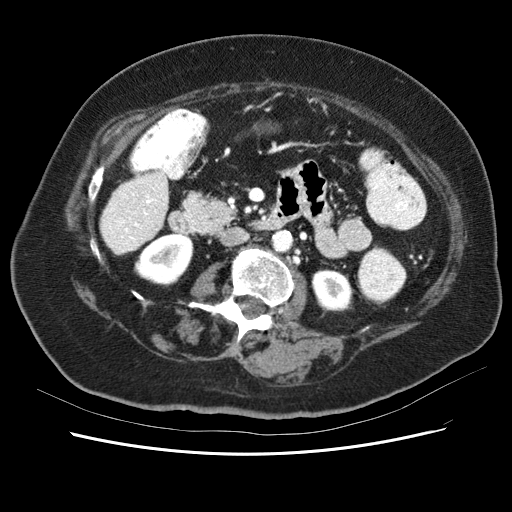
Contrast-enhanced abdominal CT (liver protocol), one axial slice; position 13 of 62 along the scan axis; 120 kVp; soft-tissue window (W 400 / L 40 HU); 512 × 512 image matrix, field of view 340 × 340 mm. From the clinical record (not read from this slice): diagnosis: hepatocellular carcinoma (patient treated with transarterial chemoembolisation; whether this scan precedes or follows treatment is not stated here); TNM stage (as recorded): Stage-I; Child-Pugh class: B; tumour size: 5.3 cm.
Structures marked on this image (semi-automatic segmentation, software-assisted and operator-edited):
- liver parenchyma outside the tumour (the mass and vessels are separate outlines, so this box may not span the whole liver): box from (x=98, y=127) to (x=201, y=258) px
- liver vessels: (x=108, y=128)–(x=200, y=250)